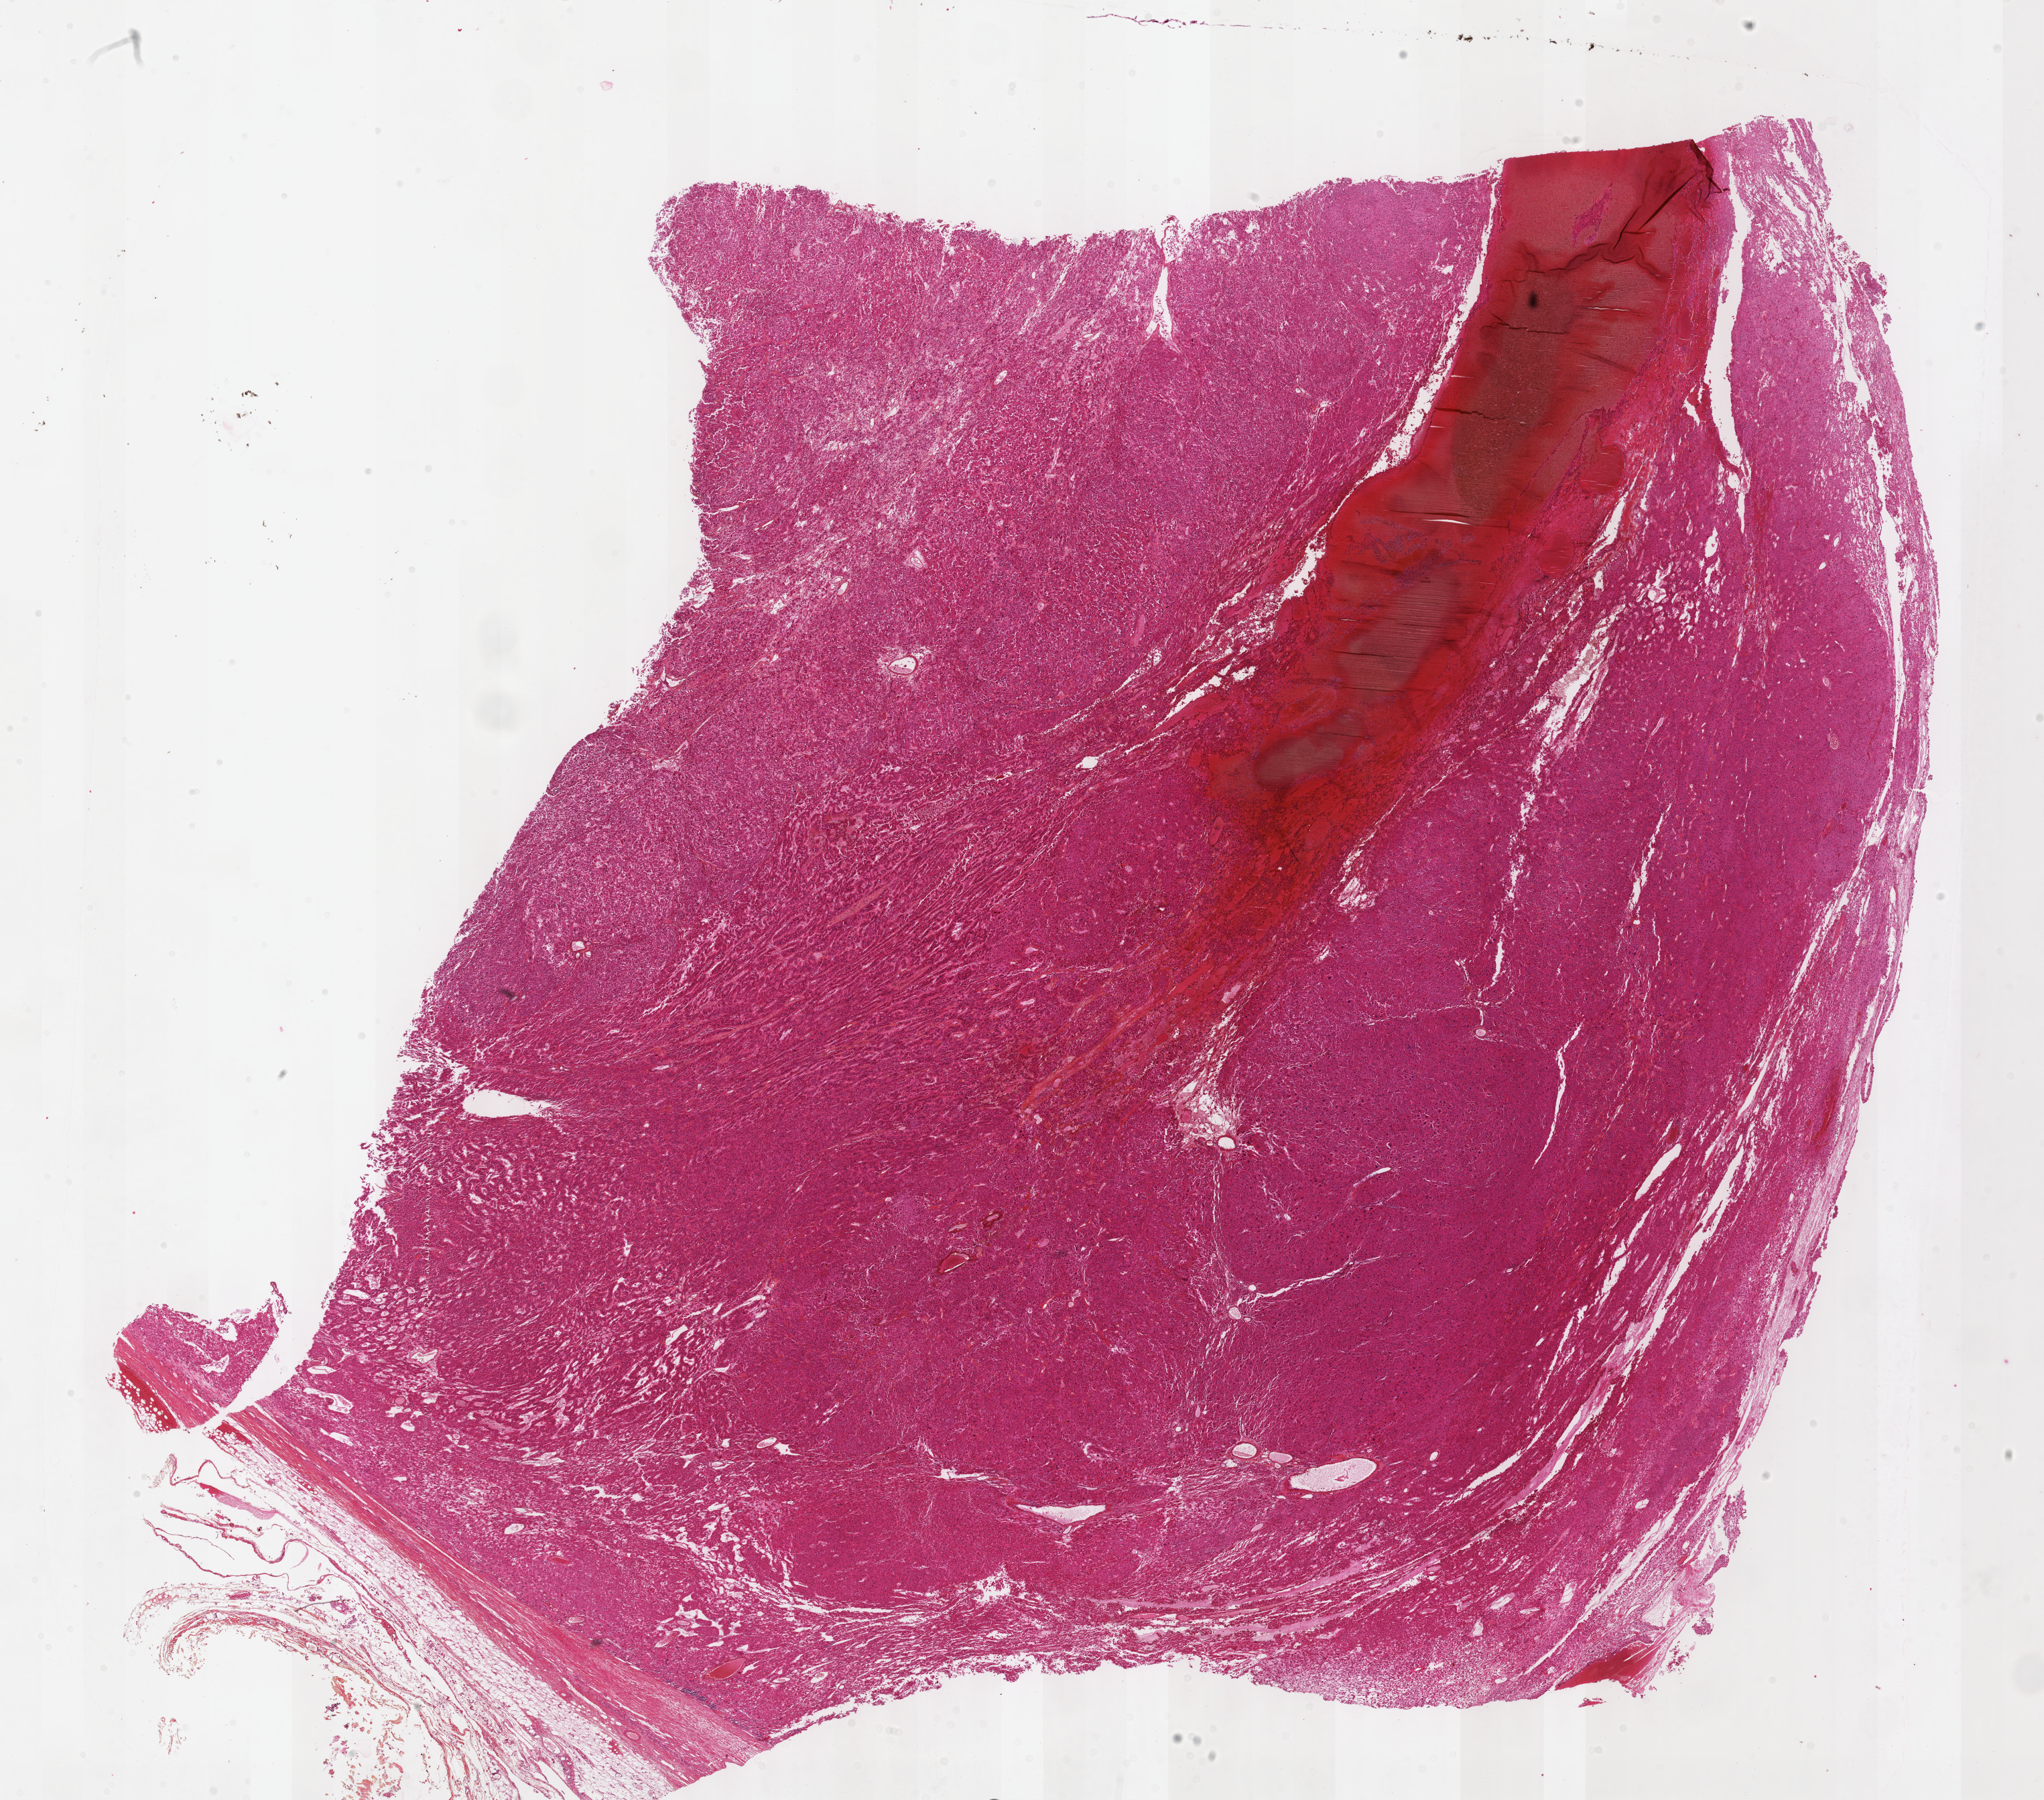
Whole-slide histology image, H&E — low-resolution overview of the scanned area, about 24.6 x 21.7 mm; formalin-fixed paraffin-embedded (FFPE) diagnostic section; adrenal cortex, primary tumour sample. Male, age 57 years at initial diagnosis.
Laterality: left. Diagnosis: Adrenal cortical carcinoma (cortex of adrenal gland).